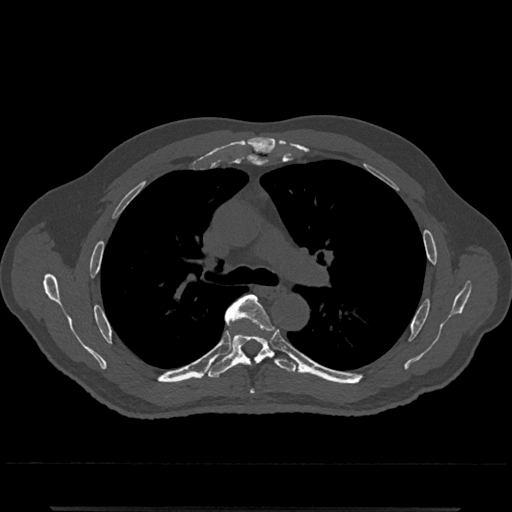
CT including the spine, one axial slice; slice 794 of 797 in the series (ordered by position); 120 kVp; bone window (W 1800 / L 400 HU); 0.5 mm slice thickness; 512 × 512 image matrix. Male patient, age 67 years. Case-level facts recorded for this patient, not image findings: primary cancer: prostate.
Outlined on this slice (semi-automatic segmentation, software-assisted and operator-edited):
- T5 vertebra: box from (x=225, y=294) to (x=270, y=328) px
- T6 vertebra: (x=206, y=304)–(x=297, y=379)